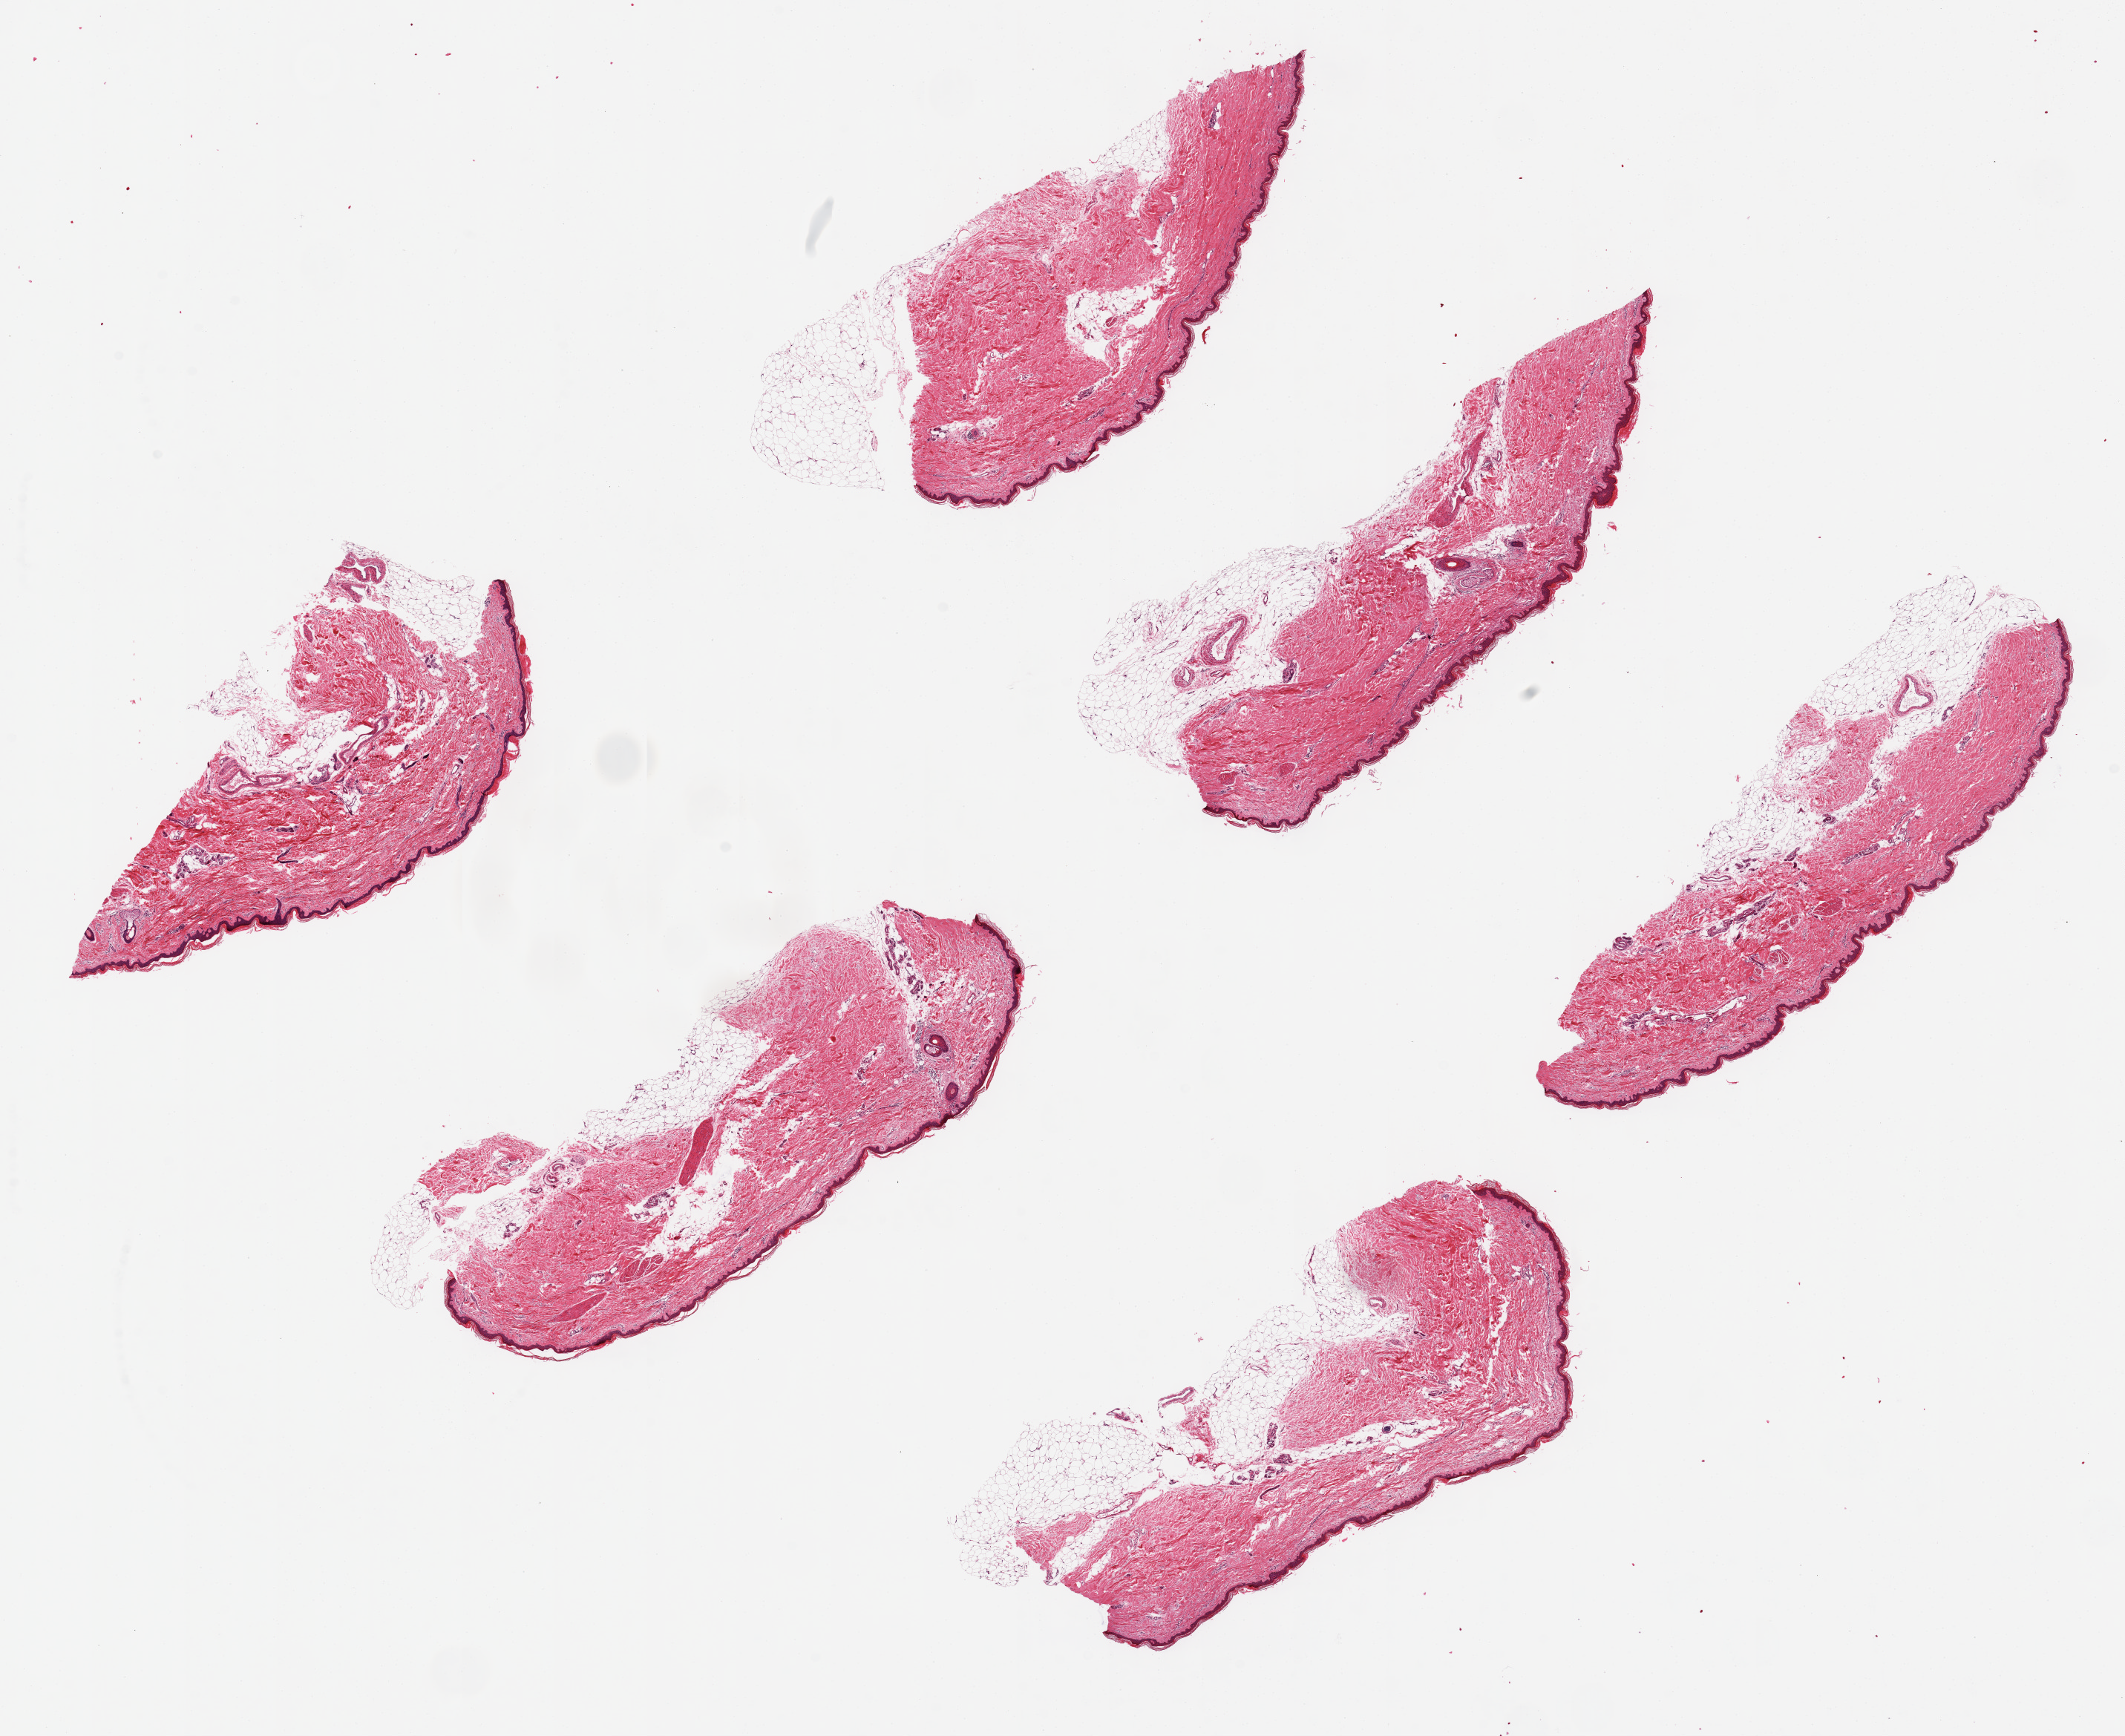
H&E whole-slide image, whole scanned area (about 22.6 x 18.5 mm) shown as a low-resolution overview, PAXgene-fixed, paraffin-embedded tissue, section of skin of lower leg (target tissue), donor tissue sample. Donor: female.
Review note (as recorded): 6 pieces up to 7x3 mm.